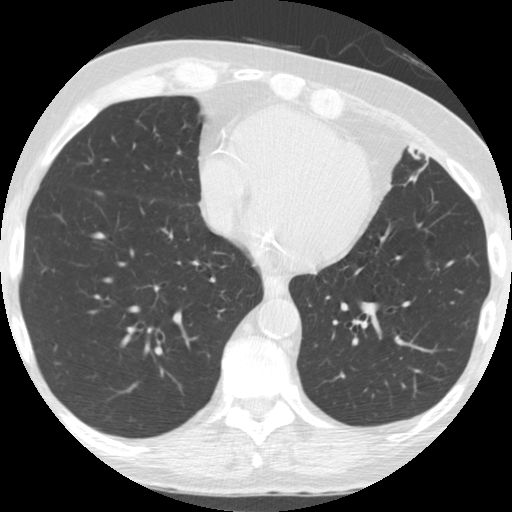
Low-dose screening chest CT, one axial slice; slice 73 of 182 in the series (ordered by position); reconstruction kernel STANDARD; 120 kVp; lung window (W 1500 / L -600 HU); 512 × 512 image matrix, field of view 320 × 320 mm.
Annotated regions visible in this slice (expert manual segmentation):
- lesion 1 (tumor, lower lobe of right lung): box from (x=98, y=192) to (x=102, y=195) px